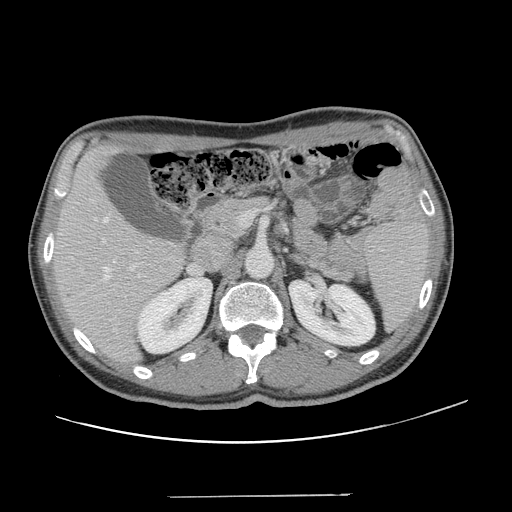
Contrast-enhanced abdominal CT, one axial slice. 120 kVp. Intravenous contrast given. Soft-tissue window (W 400 / L 40 HU). 2.5 mm slice thickness. 512 × 512 image matrix, field of view 403 × 403 mm. Male patient, age 60 years. Case-level facts recorded for this patient, not image findings: diagnosis: colorectal cancer liver metastases, imaged before liver resection; multiple liver metastases: no; largest metastasis: 2.5 cm; disease in both lobes: no.
Structures marked on this image (manually delineated by an expert):
- hepatic veins: box from (x=104, y=218) to (x=115, y=280) px
- liver: (x=54, y=149)–(x=184, y=363)
- planned liver remnant (the part of the liver to remain after resection): (x=54, y=148)–(x=184, y=361)